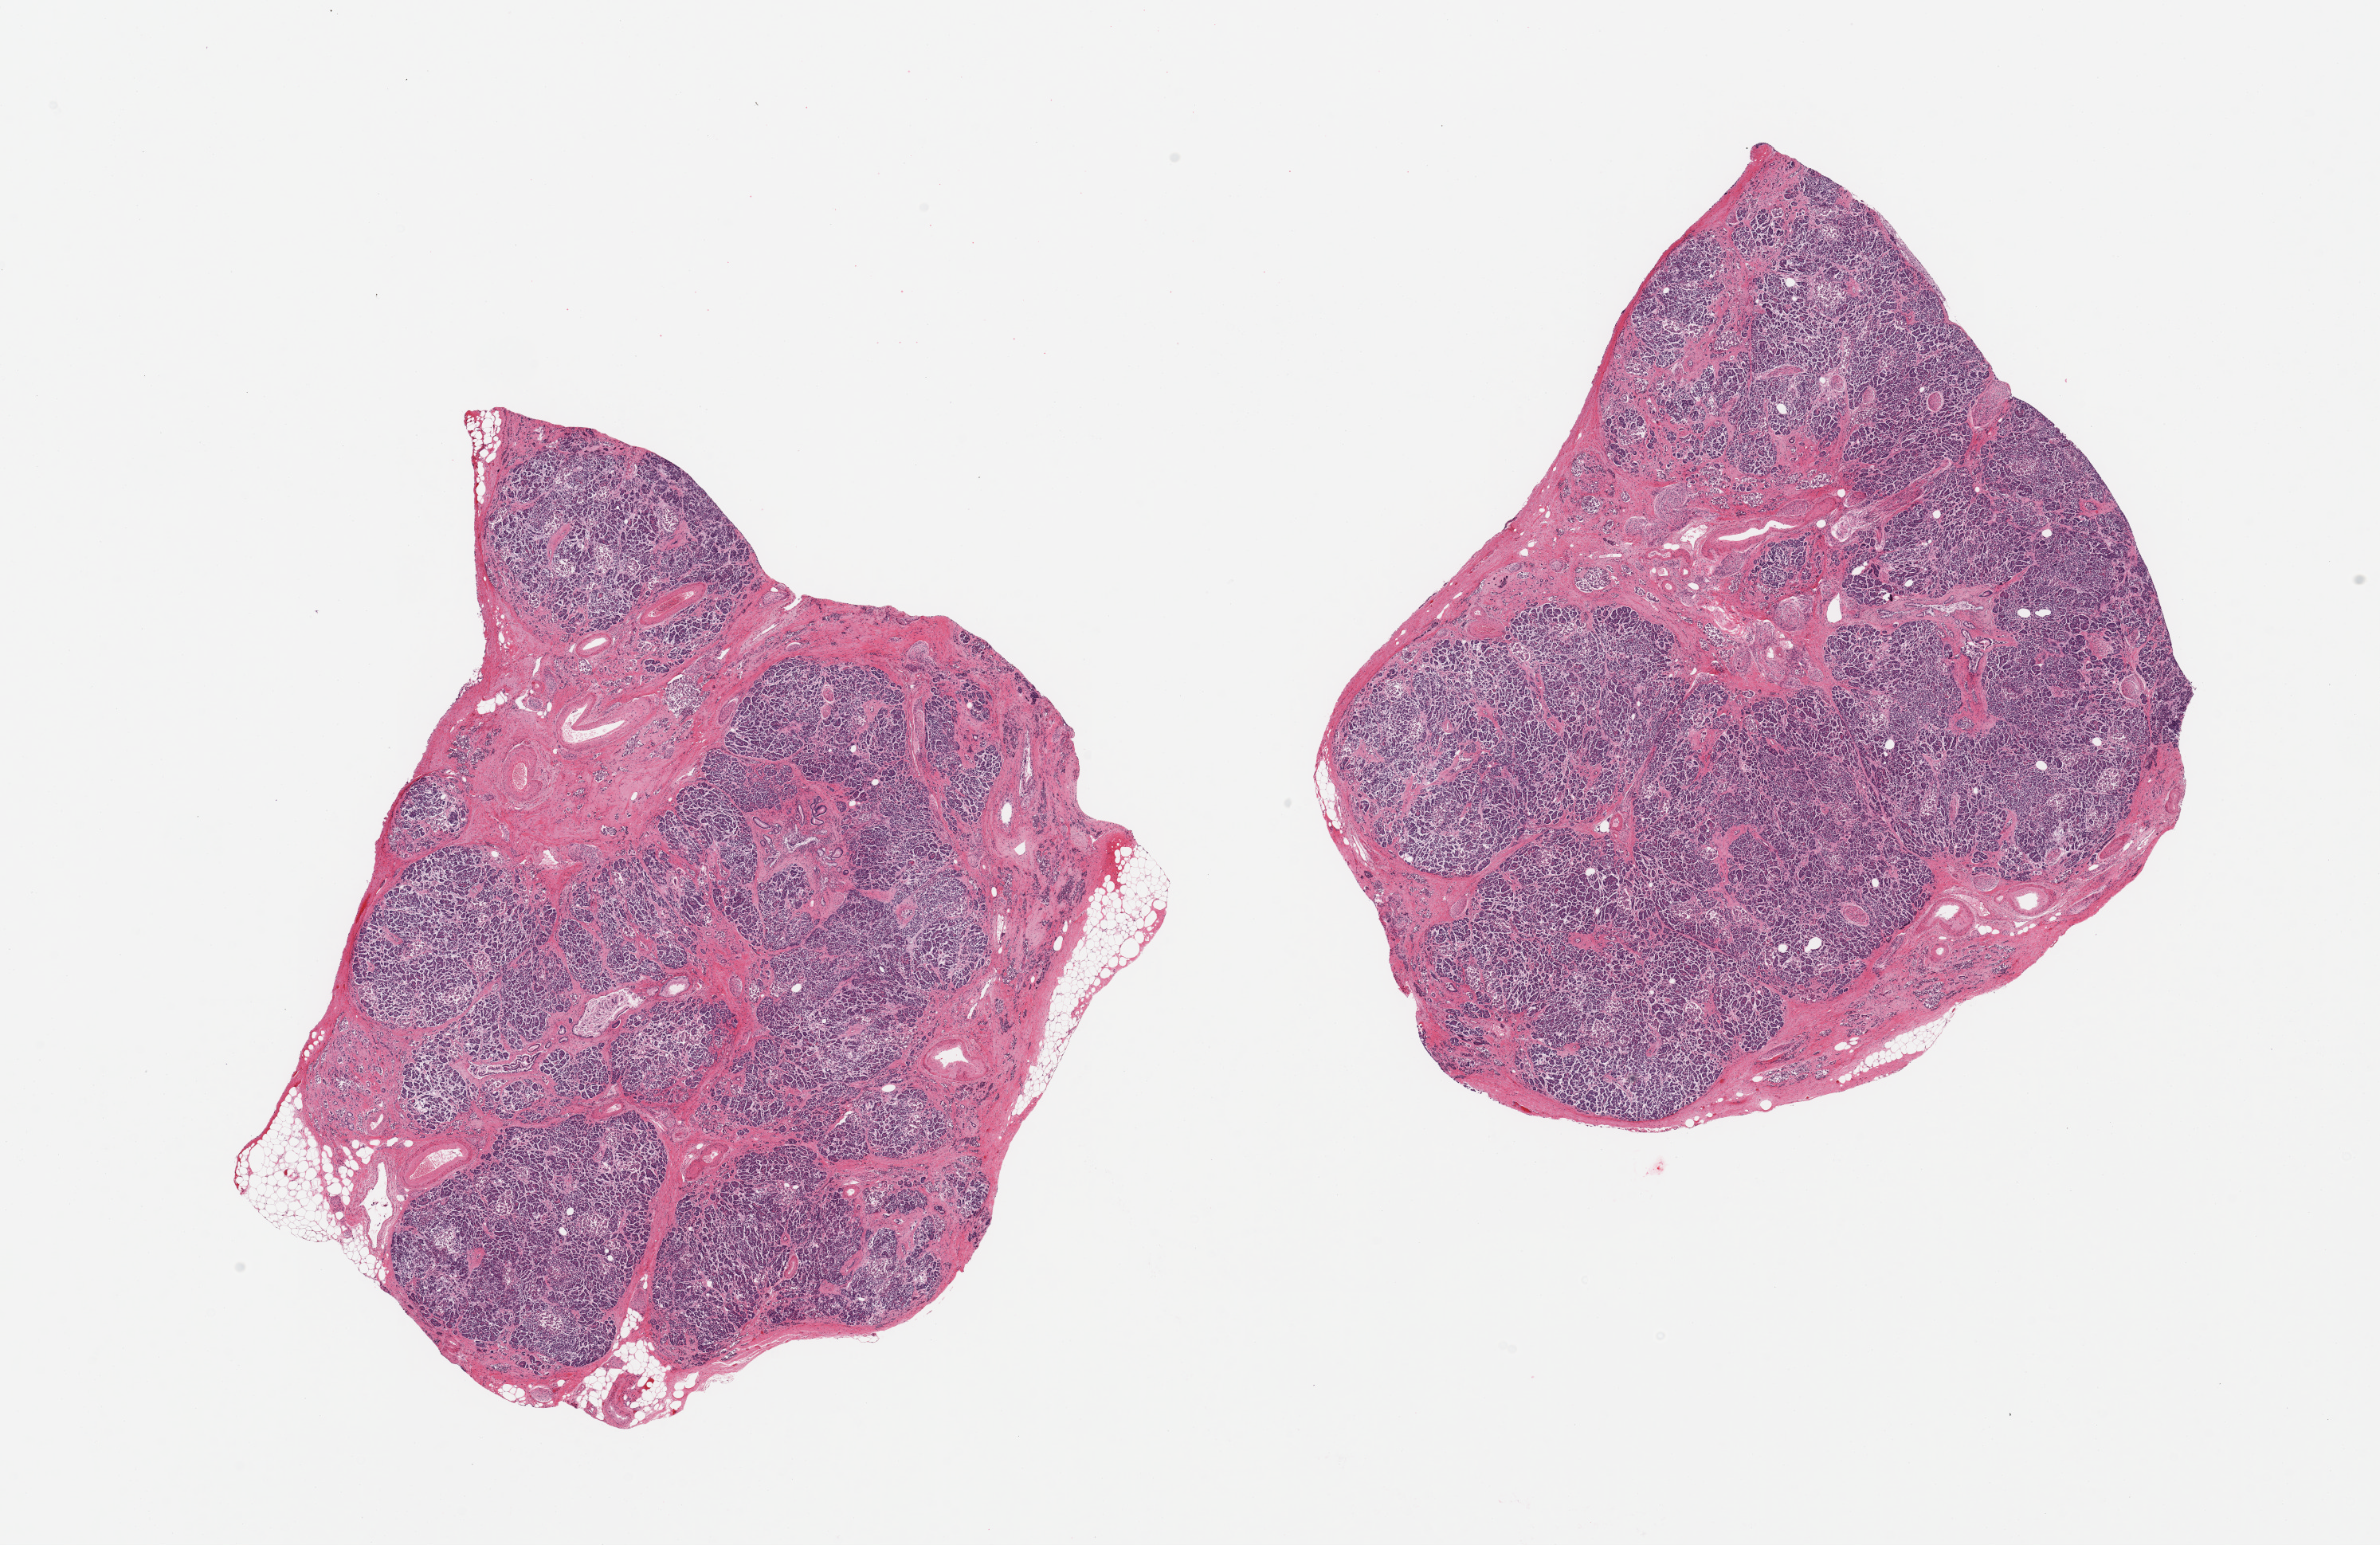
H&E whole-slide image, shown as a low-resolution overview of the whole scanned area (about 23.6 x 15.3 mm, acquisition: 20x scan); PAXgene-fixed paraffin-embedded (PFPE) section; sampled site (target tissue): pancreas; tissue donor sample. Donor: female.
Reviewer comment on this tissue sample: 2 pieces; fibrosis and atrophy, focal PanIN.